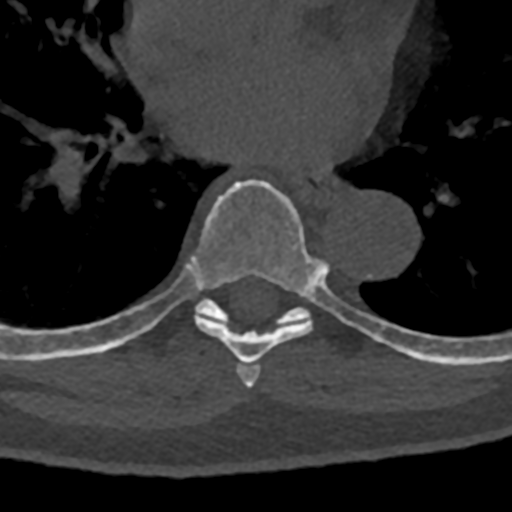
CT including the spine, one axial slice; position 748 of 797 along the scan axis; reconstruction kernel Br40s/3; 120 kVp; bone window (W 1800 / L 400 HU); 0.5 mm slice thickness; 512 × 512 image matrix. Male patient, age 74 years. From the clinical record (not read from this slice): primary cancer: renal; vertebrae with lytic lesions (as recorded): T10, L1, L2, L3, L4, L5.
Structures marked on this image (semi-automatically segmented with operator editing):
- T6 vertebra: bounding box [x1, y1, x2, y2] px = [237, 364, 261, 388]
- T7 vertebra: [71, 179, 387, 365]
- T8 vertebra: [70, 298, 432, 363]